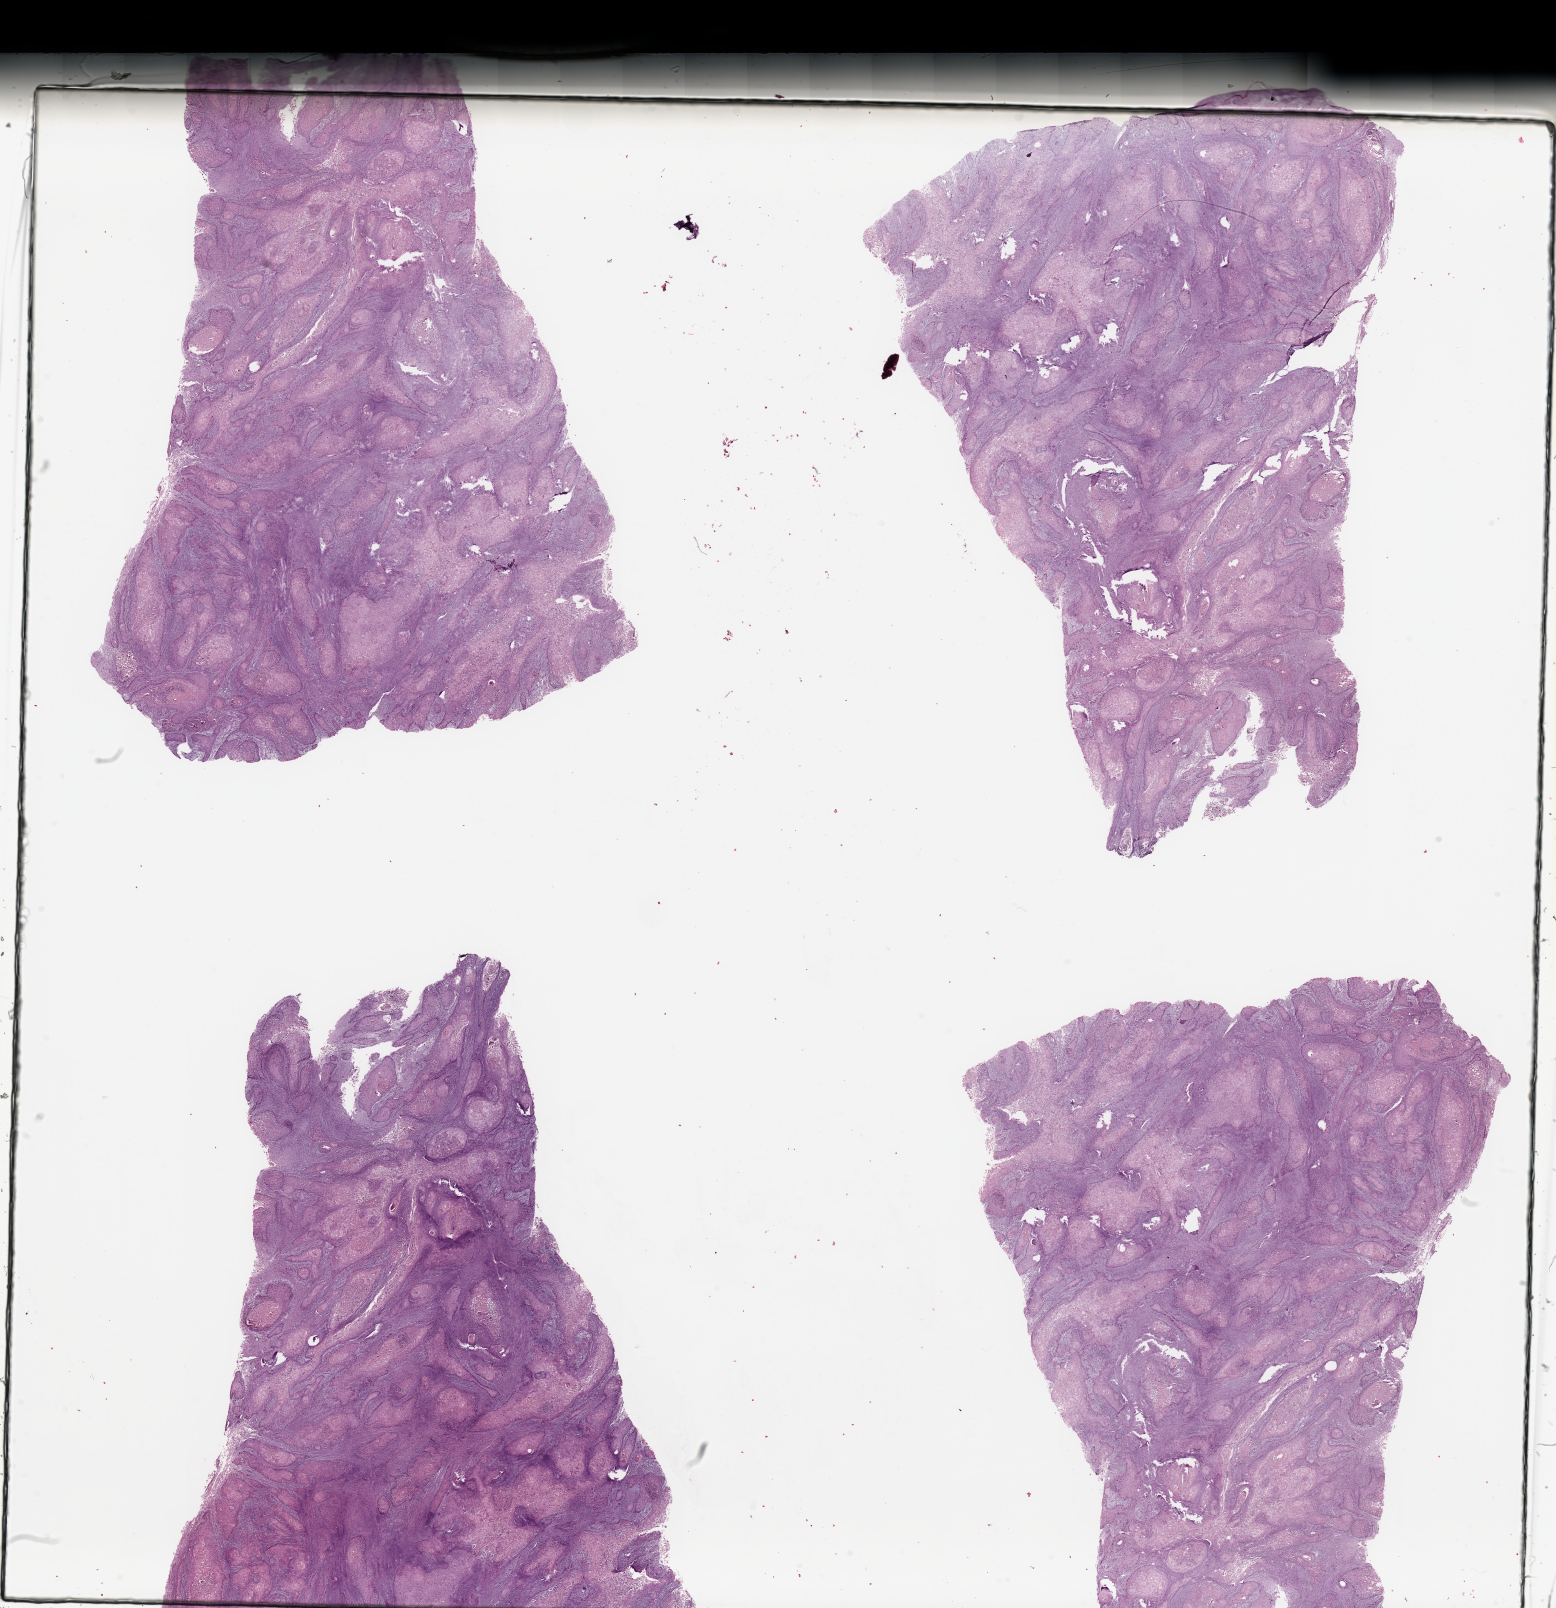
H&E-stained whole-slide image, whole scanned area (about 24.6 x 25.4 mm) shown as a low-resolution overview. Tumour tissue sample, sampled site: alveolar ridge. Patient: male, age 53 years. Histologic grade: G2 (moderately differentiated). Pathologist review of this section (percent, as recorded): tumour nuclei 85%, necrosis 7%.
Primary tumour site (as recorded): oral cavity. Histologic diagnosis: Squamous cell carcinoma, NOS (gum, NOS). AJCC pathologic stage: IVA.